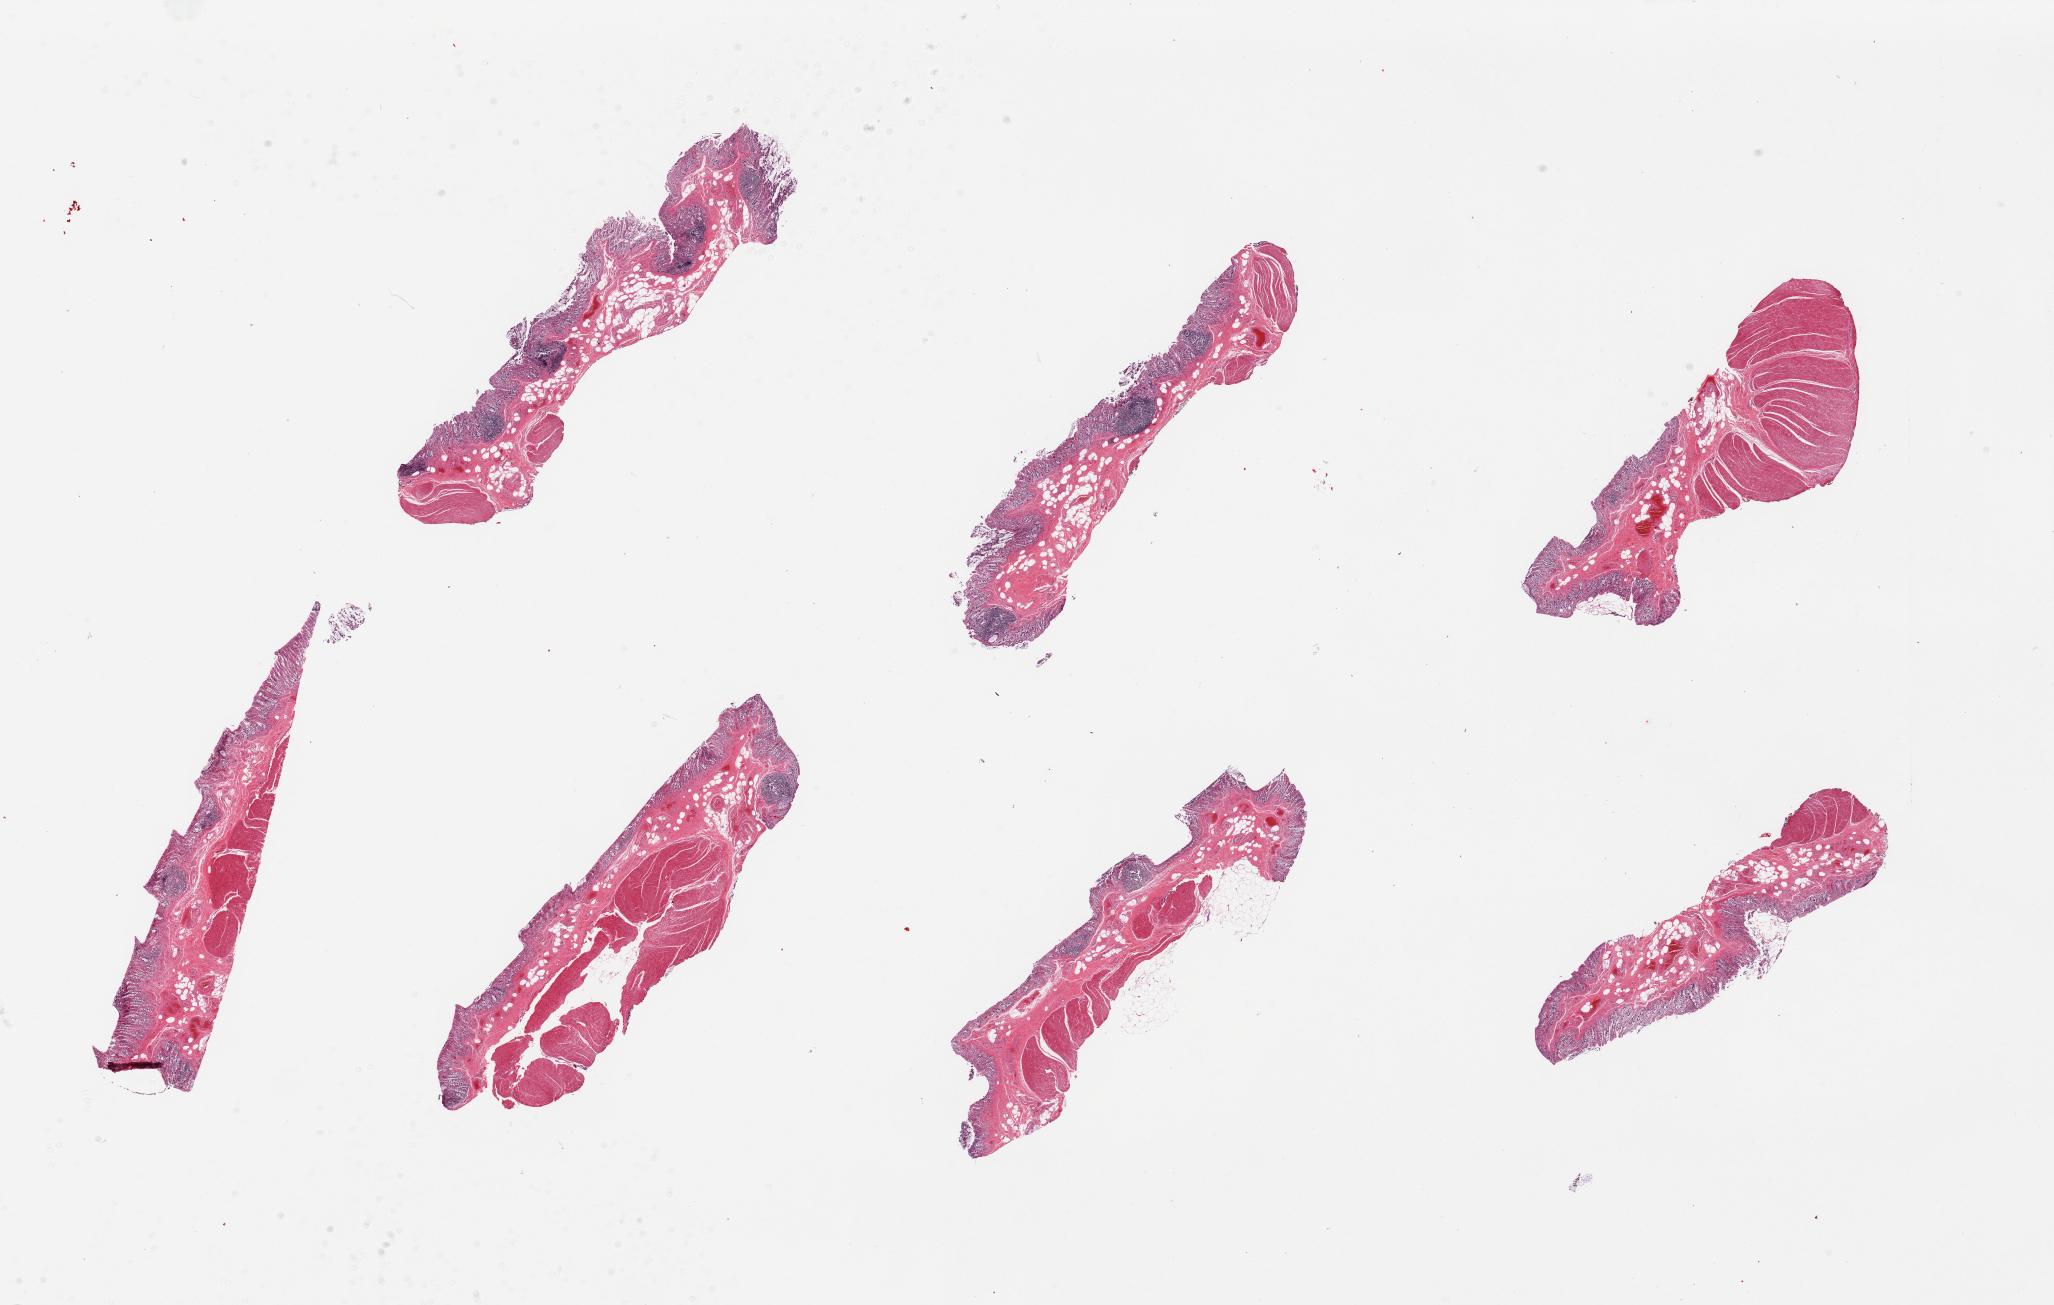
Whole-slide image, hematoxylin and eosin (H&E) stain — shown as a low-resolution overview of the whole scanned area (about 32.5 x 20.6 mm); PAXgene-fixed paraffin-embedded (PFPE) section; target tissue: transverse colon; tissue donor sample. Male donor.
Pathologist's review note for this sample: 7 pieces, muscularis and severely autolyzed mucosa.